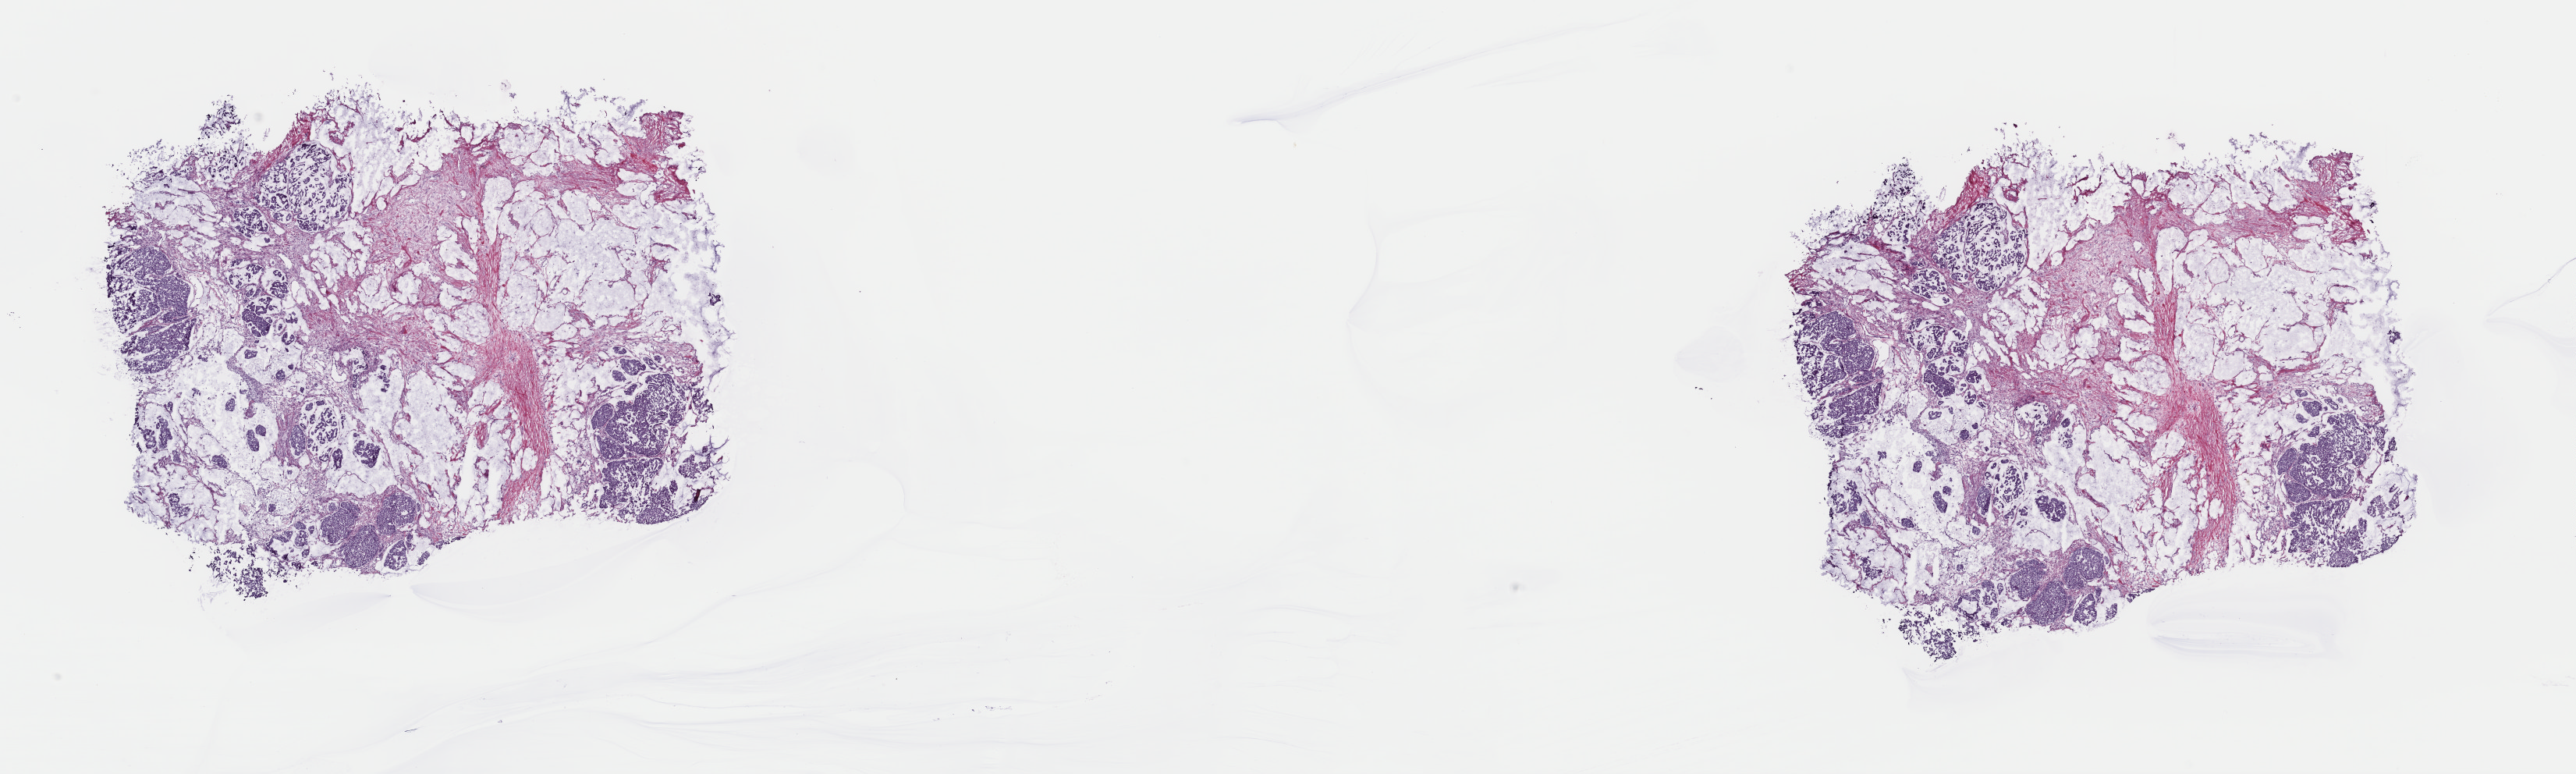
Digitized H&E tissue section (whole slide) — low-resolution overview of the scanned area, about 26.1 x 7.8 mm (acquisition: 40x scan). Frozen section from the top of the tissue portion. Breast, primary tumour sample. Patient: female, age at initial diagnosis 79 years. Pathologist review of this section (percent, as recorded): tumour cells 75%, tumour nuclei 75%, normal cells 0%, stromal cells 25%, necrosis 0%. Infiltration values recorded for this section: lymphocyte infiltration 4%, monocyte infiltration 2%, neutrophil infiltration 1%.
• lymph nodes positive (case pathology): 0 of 2 examined
• AJCC pathologic stage: IIA (7th edition)
• histologic diagnosis: Mucinous adenocarcinoma